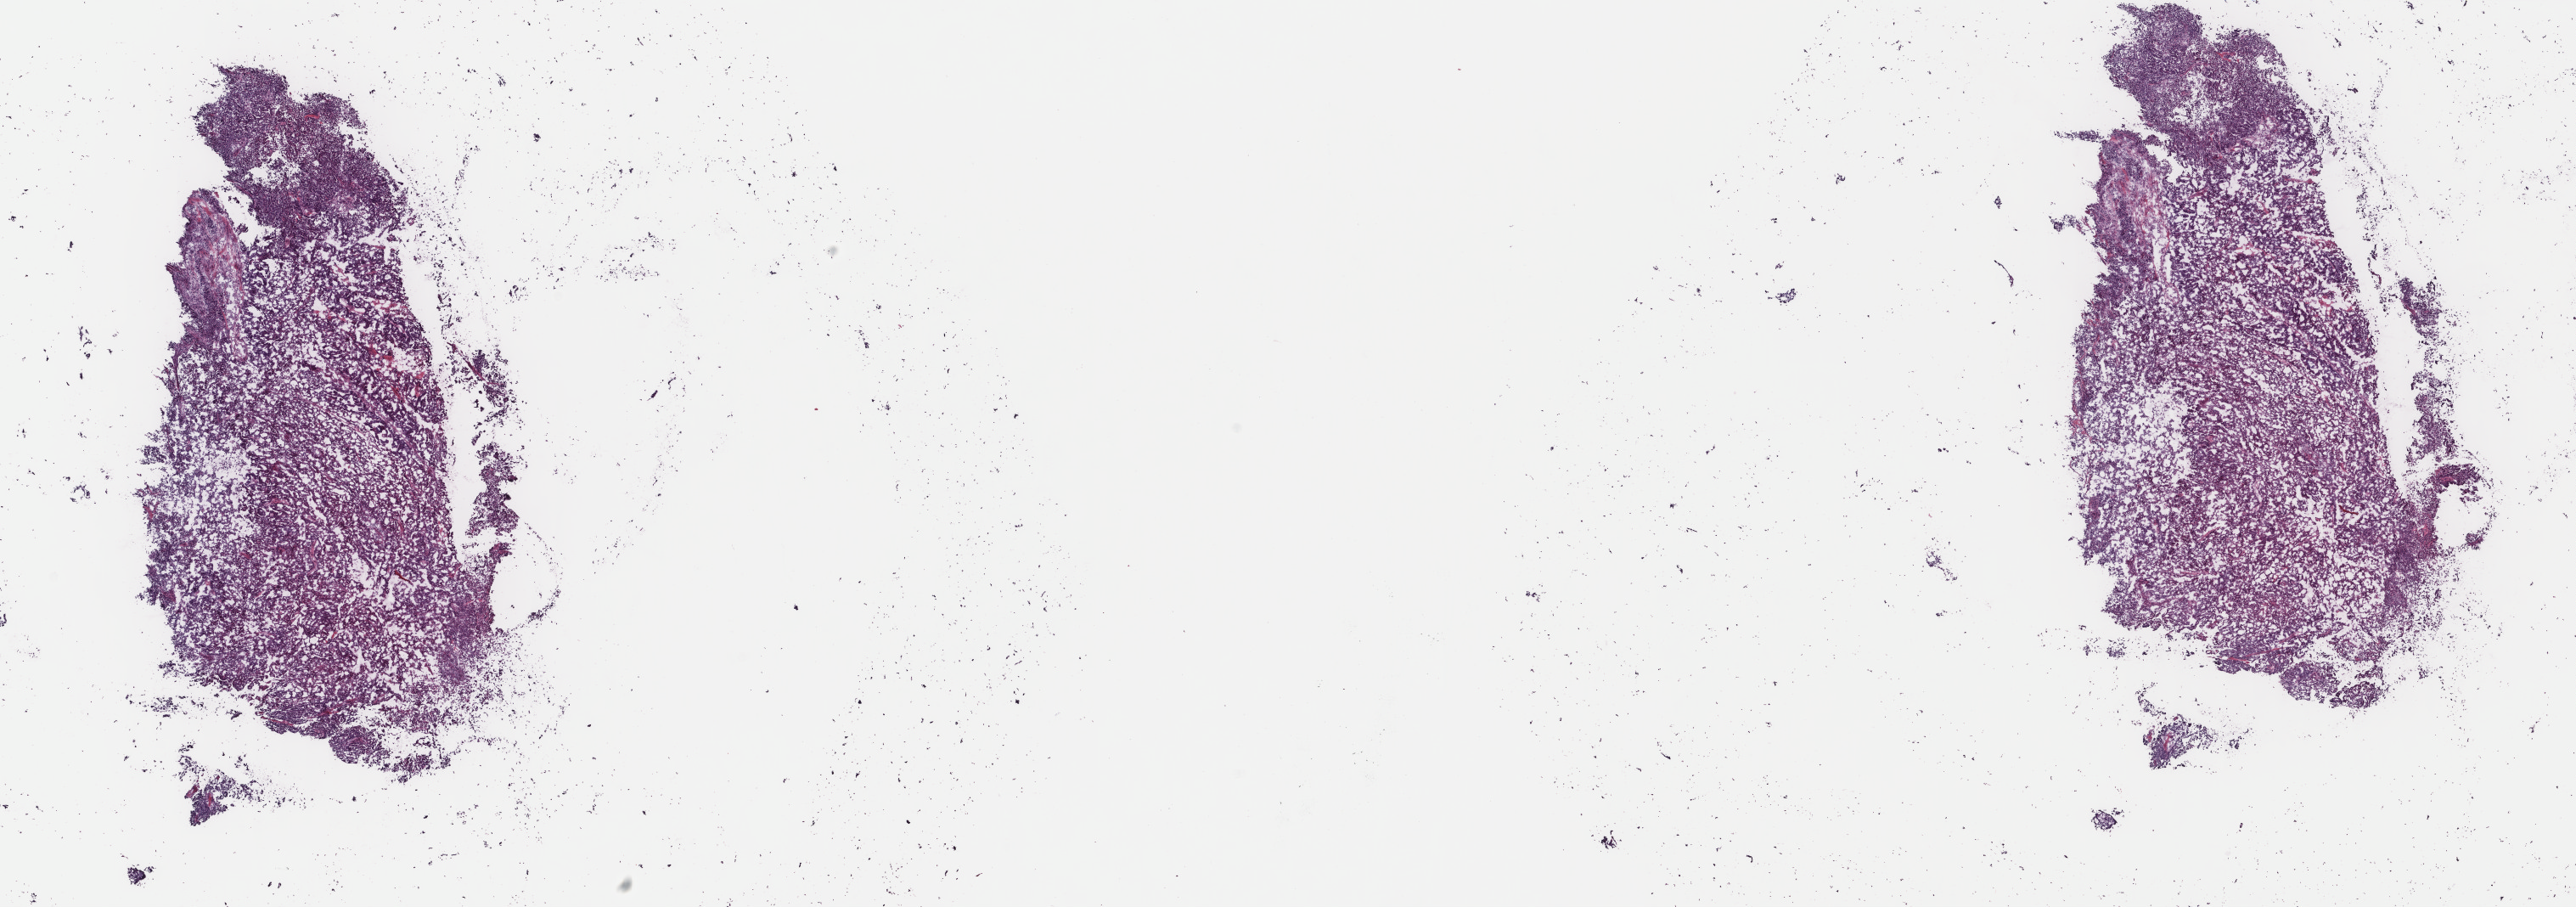
Hematoxylin and eosin (H&E) stained whole-slide image — shown as a low-resolution overview of the whole scanned area (about 24.1 x 8.5 mm), frozen section, sample: primary tumour, uterus. Patient: female, age at initial diagnosis 67 years. Histologic grade: G3 (poorly differentiated). Slide review estimates, as recorded: tumour cells 94%, tumour nuclei 97%, normal cells 0%, stromal cells 4%, necrosis 2%. Inflammatory infiltration, as recorded: lymphocyte infiltration 1%, monocyte infiltration 1%, neutrophil infiltration 0%.
FIGO stage: IIIC. Histologic diagnosis: Serous cystadenocarcinoma, NOS (endometrium).